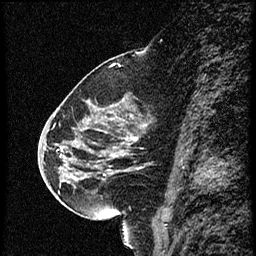
Breast MRI (dynamic contrast-enhanced), one sagittal slice. Slice 29 of 56 in the series (ordered by position). Dynamic contrast-enhanced study with each time point stored as its own series, time point 2 of 4 at this slice position (early post-contrast, ordered by acquisition time). 1.5 T. TE 4.2 ms, TR 18.9 ms. 2 mm slice thickness. 256 × 256 image matrix, field of view 200 × 200 mm. Female patient. From the clinical record (not read from this slice): setting: breast cancer imaged before/during neoadjuvant chemotherapy; receptor status: HER2-positive.
Outlined on this slice (semi-automatically segmented with operator editing):
- analysis volume of interest (the breast-tissue region the enhancement analysis was run in; not a lesion): bounding box (x1, y1, x2, y2) in pixels: (63, 80, 164, 215)
- tumour enhancement mask (voxels above the 100 % enhancement threshold inside the analysis volume of interest): (105, 138, 138, 177)